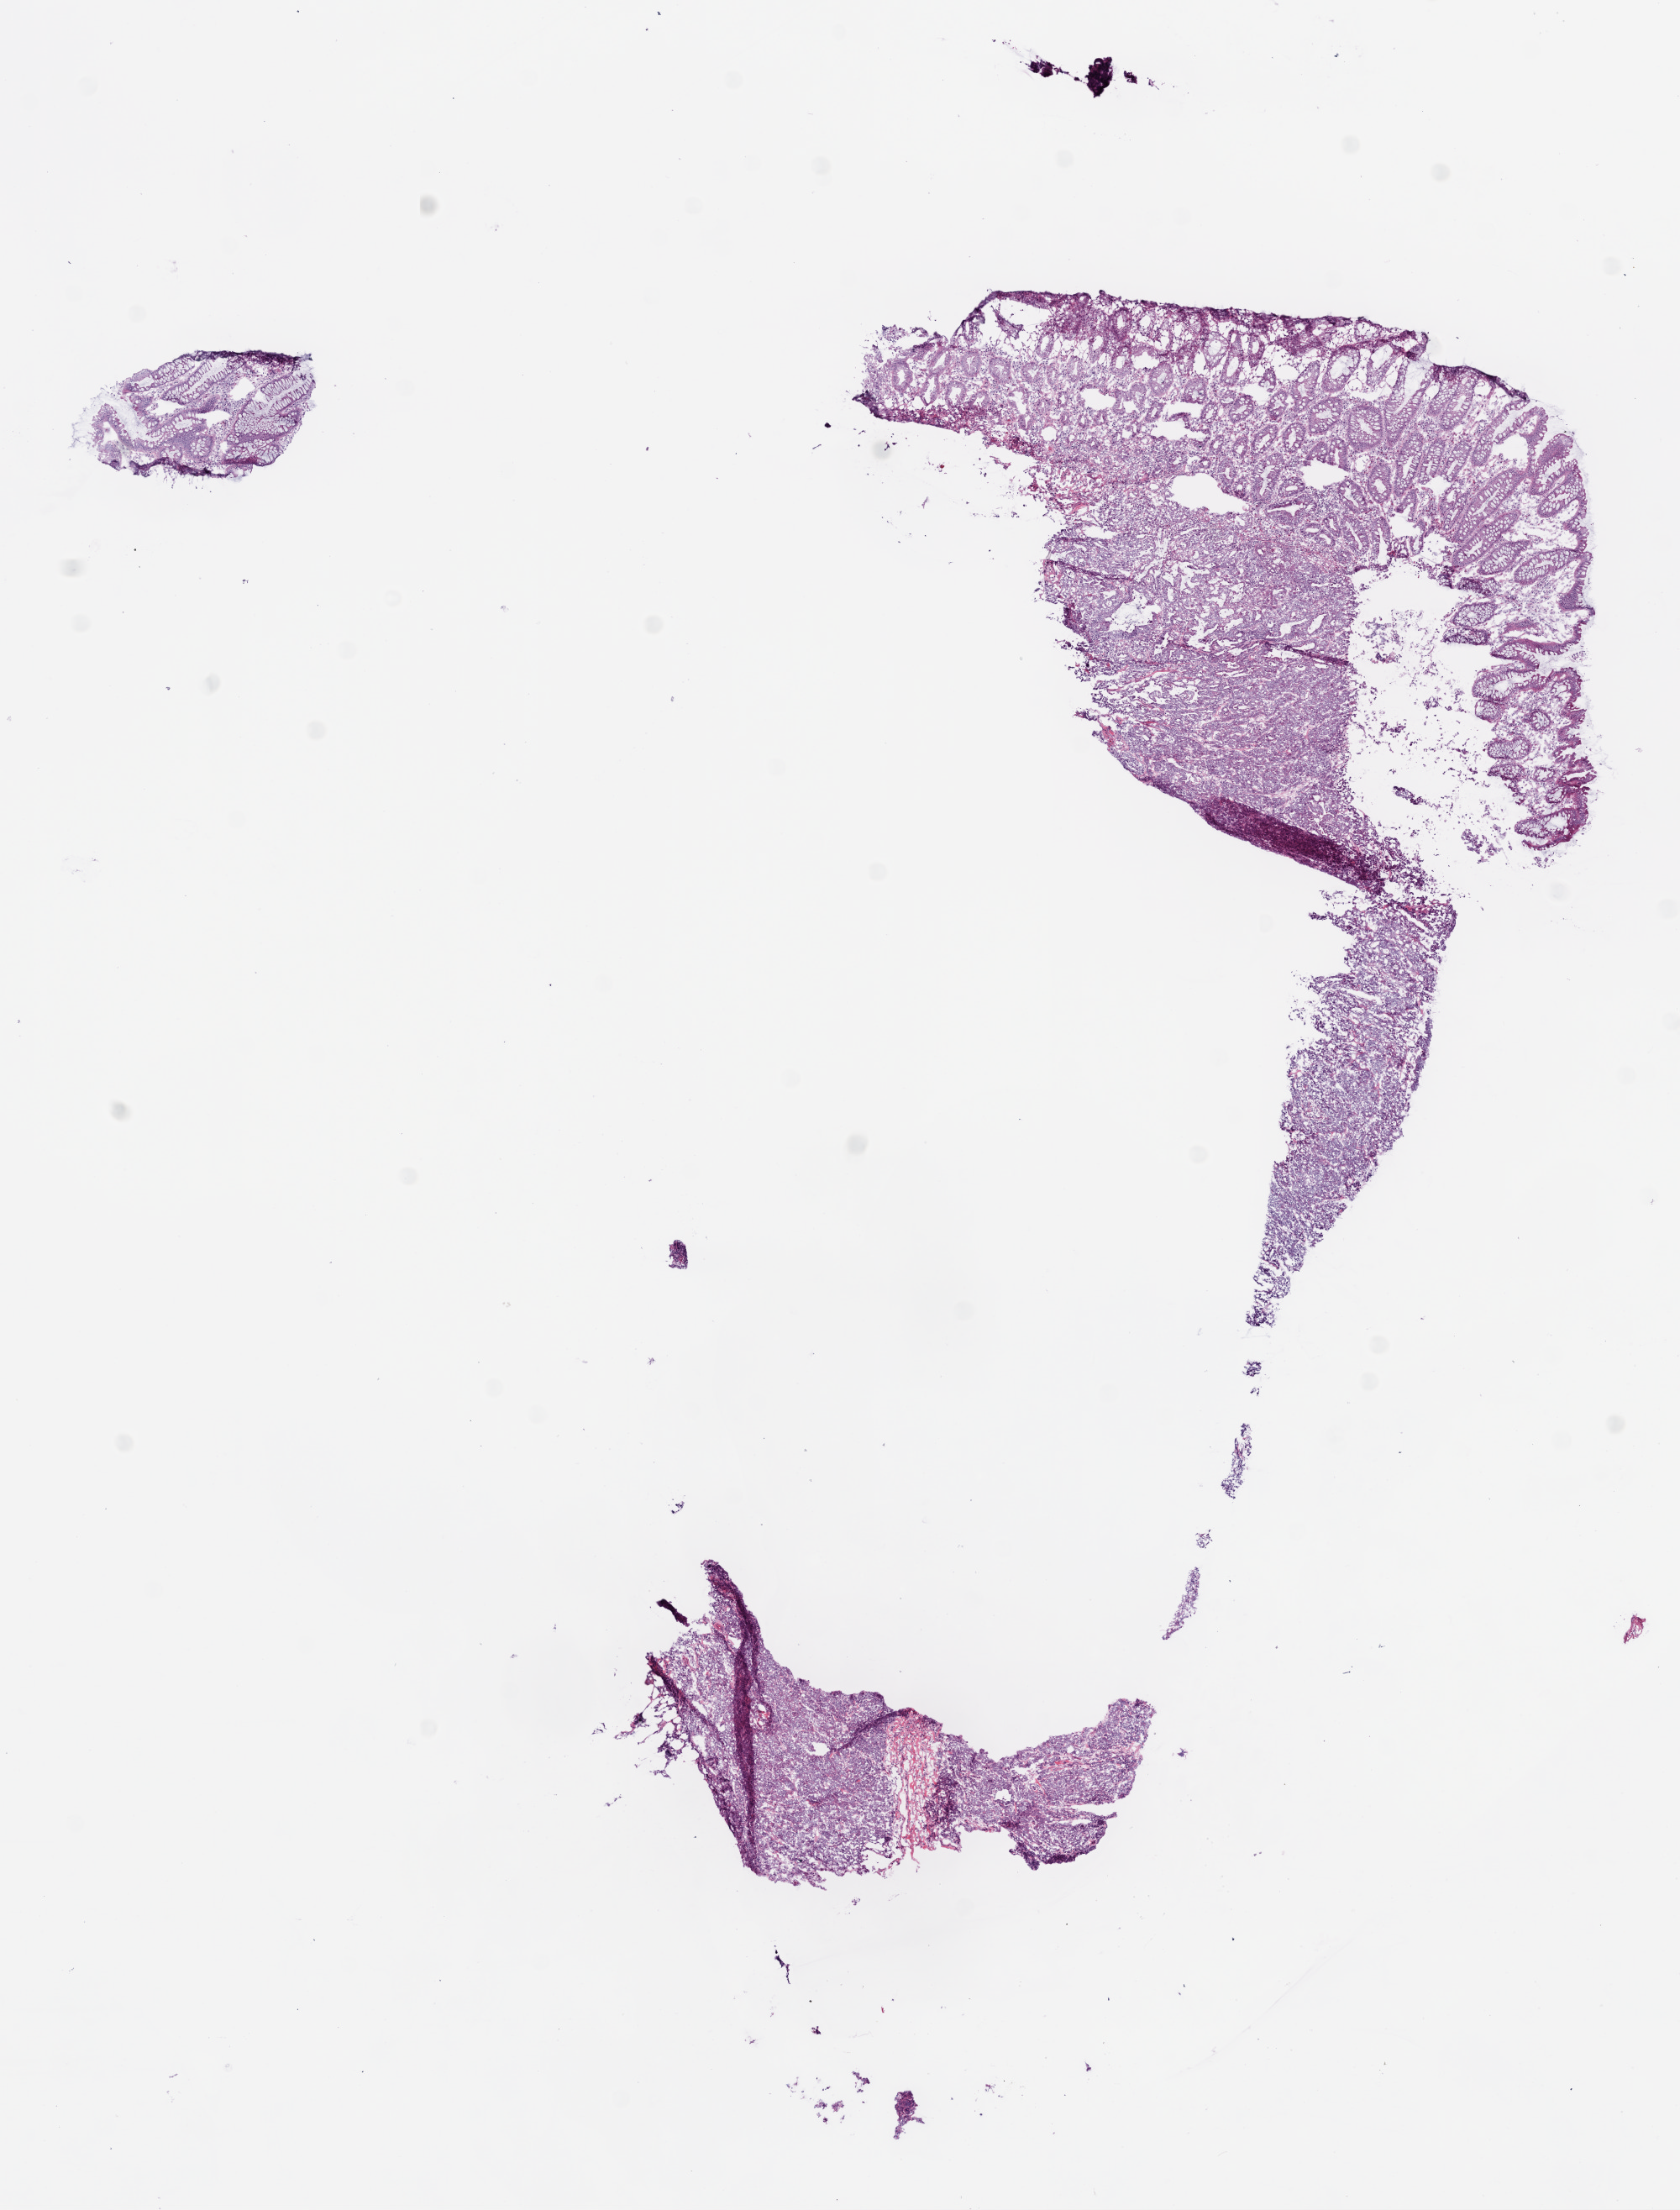
Whole-slide histology image, Hematoxylin and eosin (H&E) stained, low-resolution overview of the scanned area, about 8.0 x 10.6 mm (acquisition: 20x scan), frozen section, colon, primary tumour sample. Female patient; age at initial diagnosis 74 years. Composition of this section per pathologist review: tumour cells 80%, tumour nuclei 90%, normal cells 20%, stromal cells 0%, necrosis 0%.
* AJCC pathologic stage: III (5th edition)
* lymph nodes positive (case pathology): 7 of 26 examined
* histologic diagnosis: Mucinous adenocarcinoma